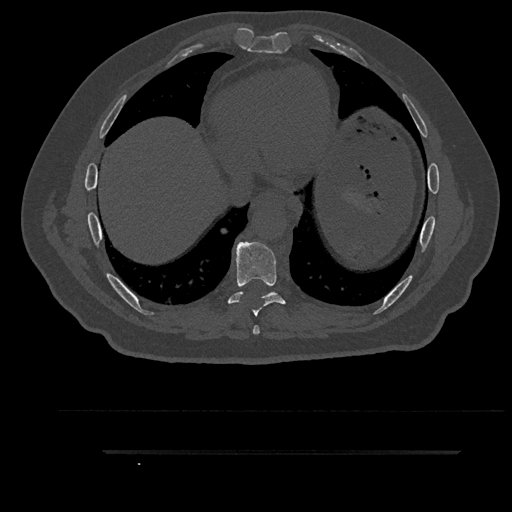
CT including the spine, one axial slice. Slice 474 of 797 in the series (ordered by position). 120 kVp. Bone window (W 1800 / L 400 HU). 512 × 512 image matrix, field of view 432 × 432 mm. Male patient, age 63 years. Case-level facts recorded for this patient, not image findings: primary cancer: renal; vertebrae with lytic lesions (as recorded): T8.
Outlined on this slice (semi-automatically segmented with operator editing):
- T7 vertebra: box from (x=252, y=325) to (x=260, y=335) px
- T8 vertebra: (x=227, y=242)–(x=293, y=316)